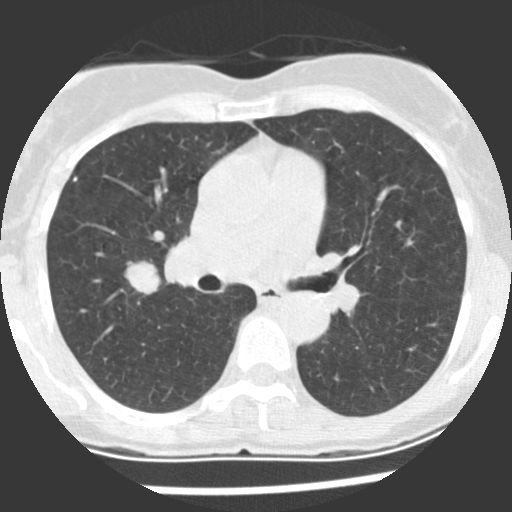
Low-dose screening chest CT, one axial slice. Position 126 of 225 along the scan axis. 120 kVp. Lung window (W 1500 / L -600 HU). 2.5 mm slice thickness. 512 × 512 image matrix, field of view 270 × 270 mm.
Structures marked on this image (manually delineated by an expert):
- lesion 1 (tumor, upper lobe of right lung): box from (x=124, y=261) to (x=161, y=295) px